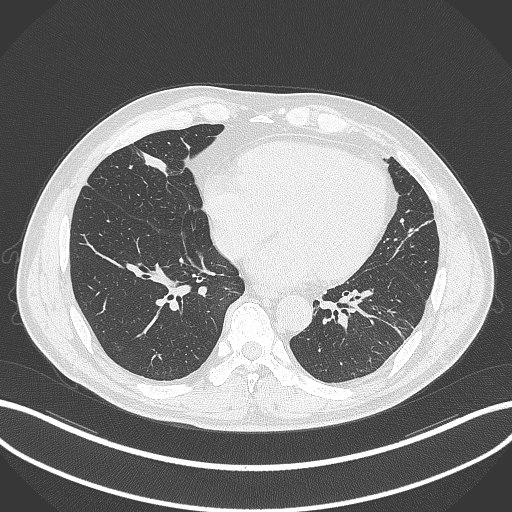
Chest CT, one axial slice; slice 93 of 399 in the series (ordered by position); reconstruction kernel B70f; lung window (W 1500 / L -600 HU); 512 × 512 image matrix, field of view 400 × 400 mm. Male patient, age 59 years. Case-level facts recorded for this patient, not image findings: clinical TNM (as recorded): T2a N1 M0.
Outlined on this slice (bounding box drawn by a radiologist):
- lung tumour (recorded histology: adenocarcinoma): bounding box (x1, y1, x2, y2) in pixels: (132, 147, 179, 178)